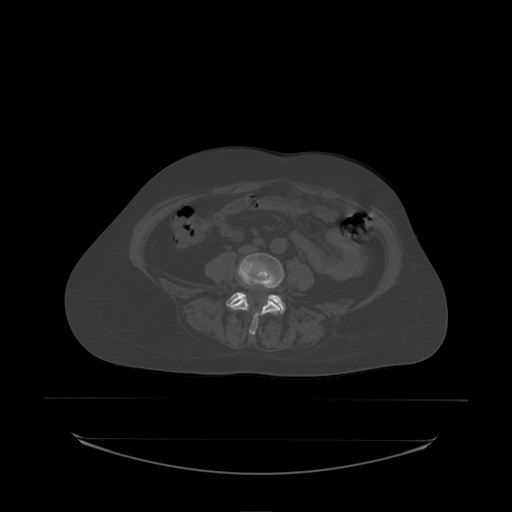
CT including the spine, one axial slice. Slice 46 of 242 in the series (ordered by position). Bone window (W 1800 / L 400 HU). 512 × 512 image matrix, field of view 500 × 500 mm. Female patient, age 53 years. From the clinical record (not read from this slice): primary cancer: lung; vertebrae with lytic lesions (as recorded): T7, L1.
Structures marked on this image (semi-automatic segmentation, software-assisted and operator-edited):
- L4 vertebra: bounding box <230,253,285,335> (left, top, right, bottom; pixels)
- L5 vertebra: <226,293,286,314>